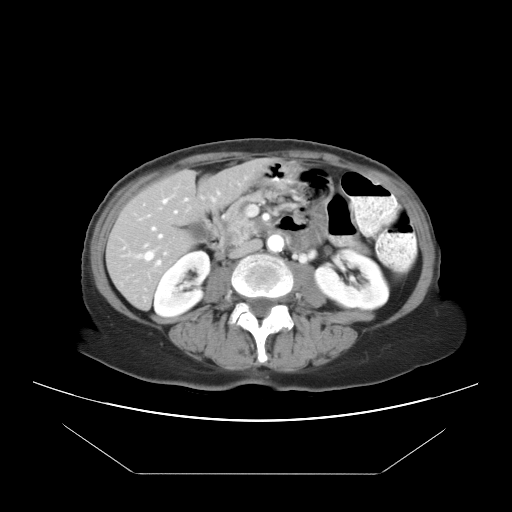
Contrast-enhanced abdominal CT, one axial slice; position 7 of 21 along the scan axis; 120 kVp; soft-tissue window (W 400 / L 40 HU); 512 × 512 image matrix. Female patient, age 72 years. From the clinical record (not read from this slice): diagnosis: colorectal cancer liver metastases, imaged before liver resection; multiple liver metastases: yes; largest metastasis: 4 cm; disease in both lobes: yes.
Annotated regions visible in this slice (expert manual segmentation):
- hepatic veins: box from (x=132, y=197) to (x=178, y=262) px
- liver: (x=107, y=162)–(x=263, y=308)
- planned liver remnant (the part of the liver to remain after resection): (x=107, y=162)–(x=263, y=292)
- portal vein (with intrahepatic branches): (x=144, y=193)–(x=220, y=264)